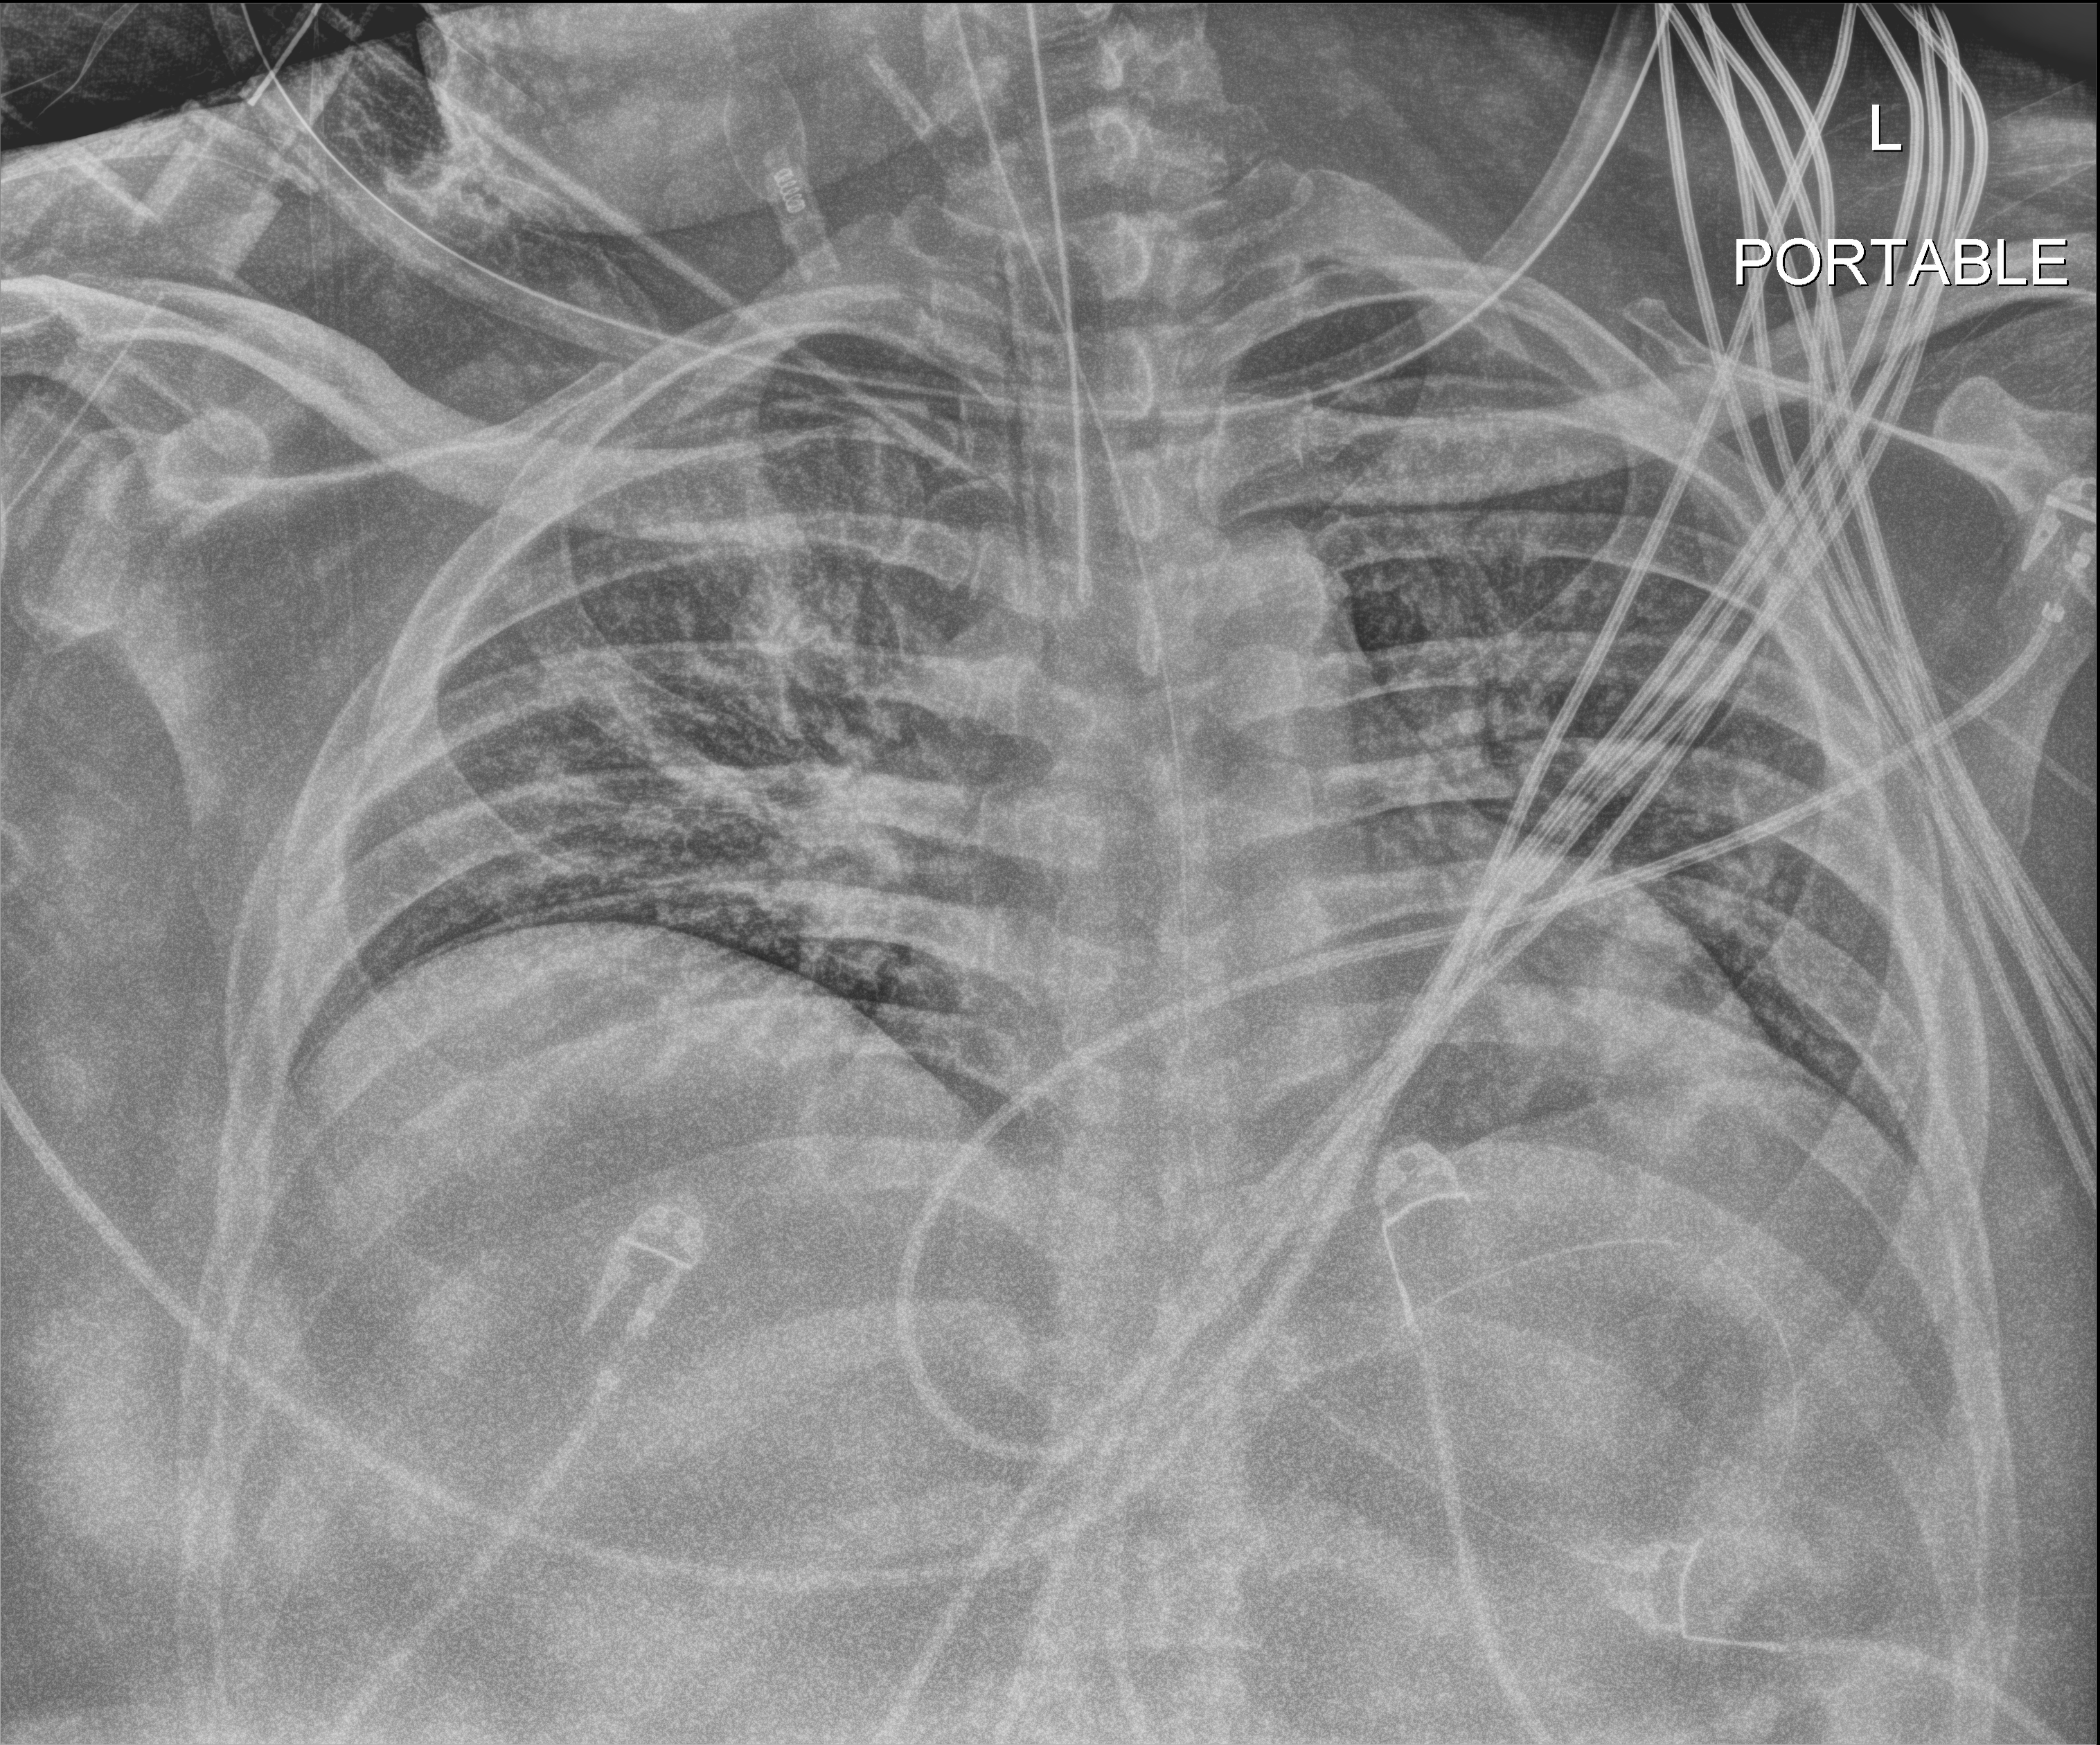
Chest X-ray (portable). Male patient hospitalised with COVID-19, age 18–59 years.
From the hospital-stay record, not from the radiograph (when in the stay this image was taken is not recorded):
- diabetes (admission record): yes
- COPD (admission record): yes